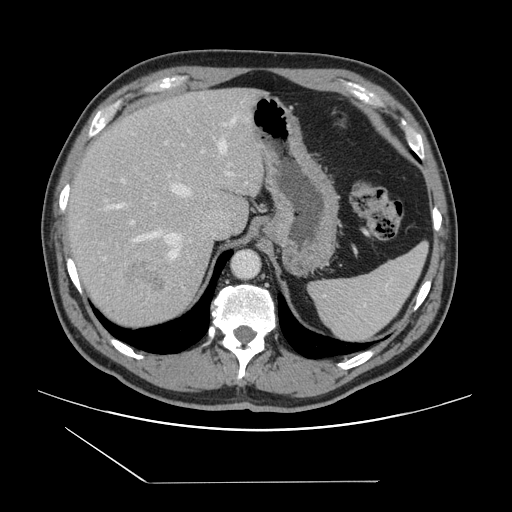
Contrast-enhanced abdominal CT, one axial slice. Position 110 of 157 along the scan axis. Intravenous contrast given. Soft-tissue window (W 400 / L 40 HU). 2.5 mm slice thickness. 512 × 512 image matrix, field of view 407 × 407 mm. Male patient, age 61 years. From the clinical record (not read from this slice): diagnosis: colorectal cancer liver metastases, imaged before liver resection; multiple liver metastases: yes; largest metastasis: 5.5 cm; disease in both lobes: yes.
Structures marked on this image (expert manual segmentation):
- hepatic veins: bounding box [x1, y1, x2, y2] px = [112, 116, 237, 263]
- liver: [67, 89, 264, 329]
- planned liver remnant (the part of the liver to remain after resection): [67, 89, 237, 230]
- portal vein (with intrahepatic branches): [122, 142, 233, 224]
- liver metastasis: [120, 257, 172, 311]